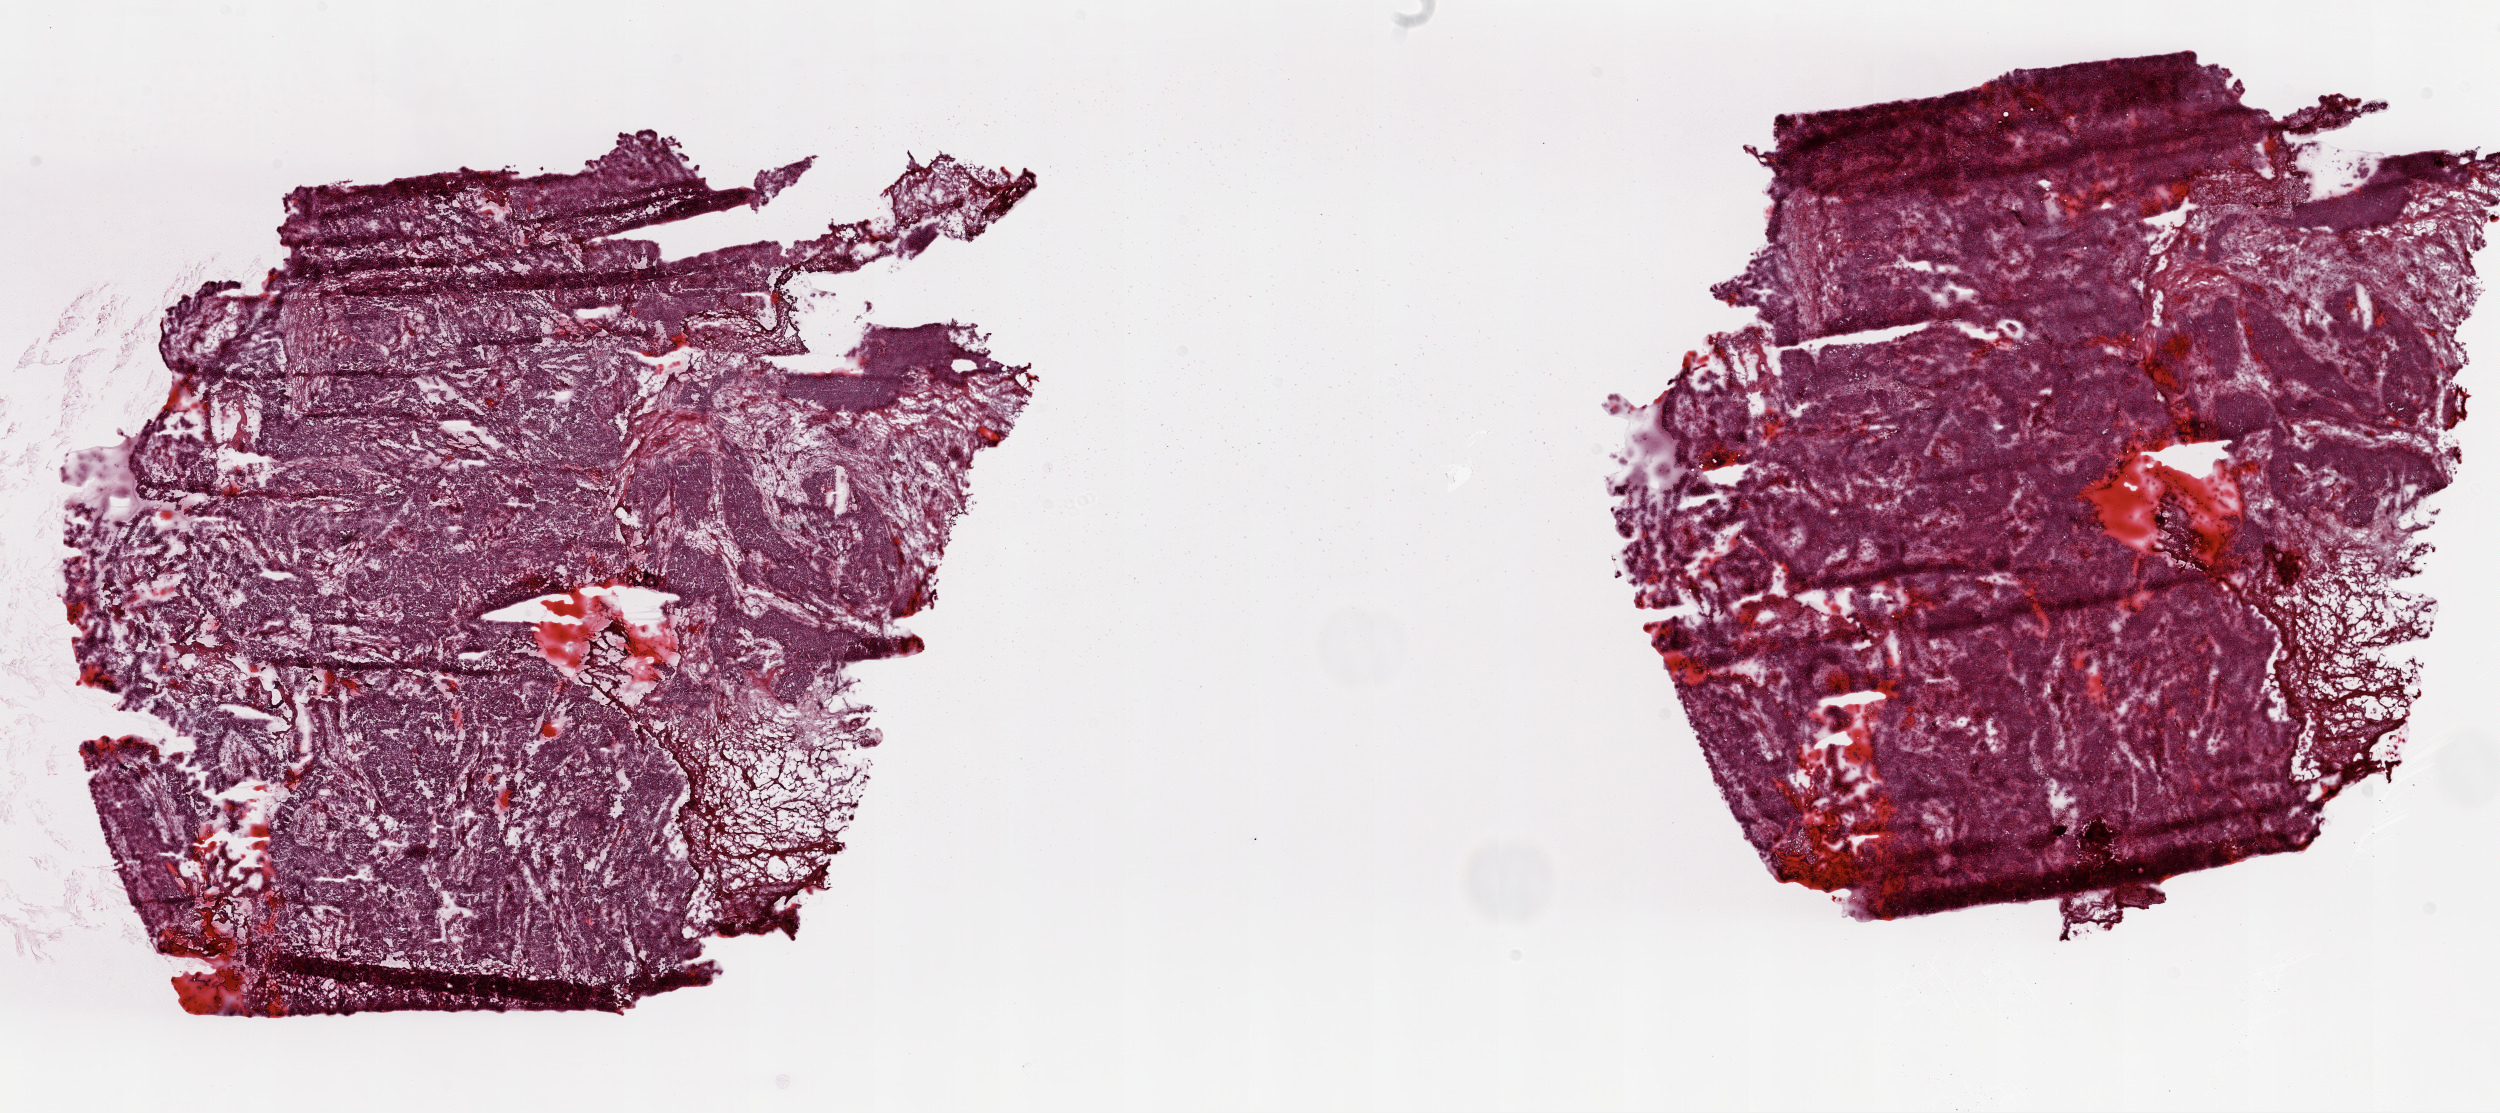
H&E-stained whole-slide image — low-resolution overview of the scanned area, about 20.1 x 8.9 mm (from a 20x scan); frozen section from the top of the tissue portion; primary tumour sample from the ovary. Patient: female, age at initial diagnosis 59 years. Histologic grade: G3 (poorly differentiated). Composition of this section per pathologist review: tumour cells 90%, tumour nuclei 90%, normal cells 0%, stromal cells 0%, necrosis 10%. Infiltration values recorded for this section: lymphocyte infiltration 0%, monocyte infiltration 0%, neutrophil infiltration 5%.
FIGO stage: IIIC. Histologic diagnosis: Serous cystadenocarcinoma, NOS.